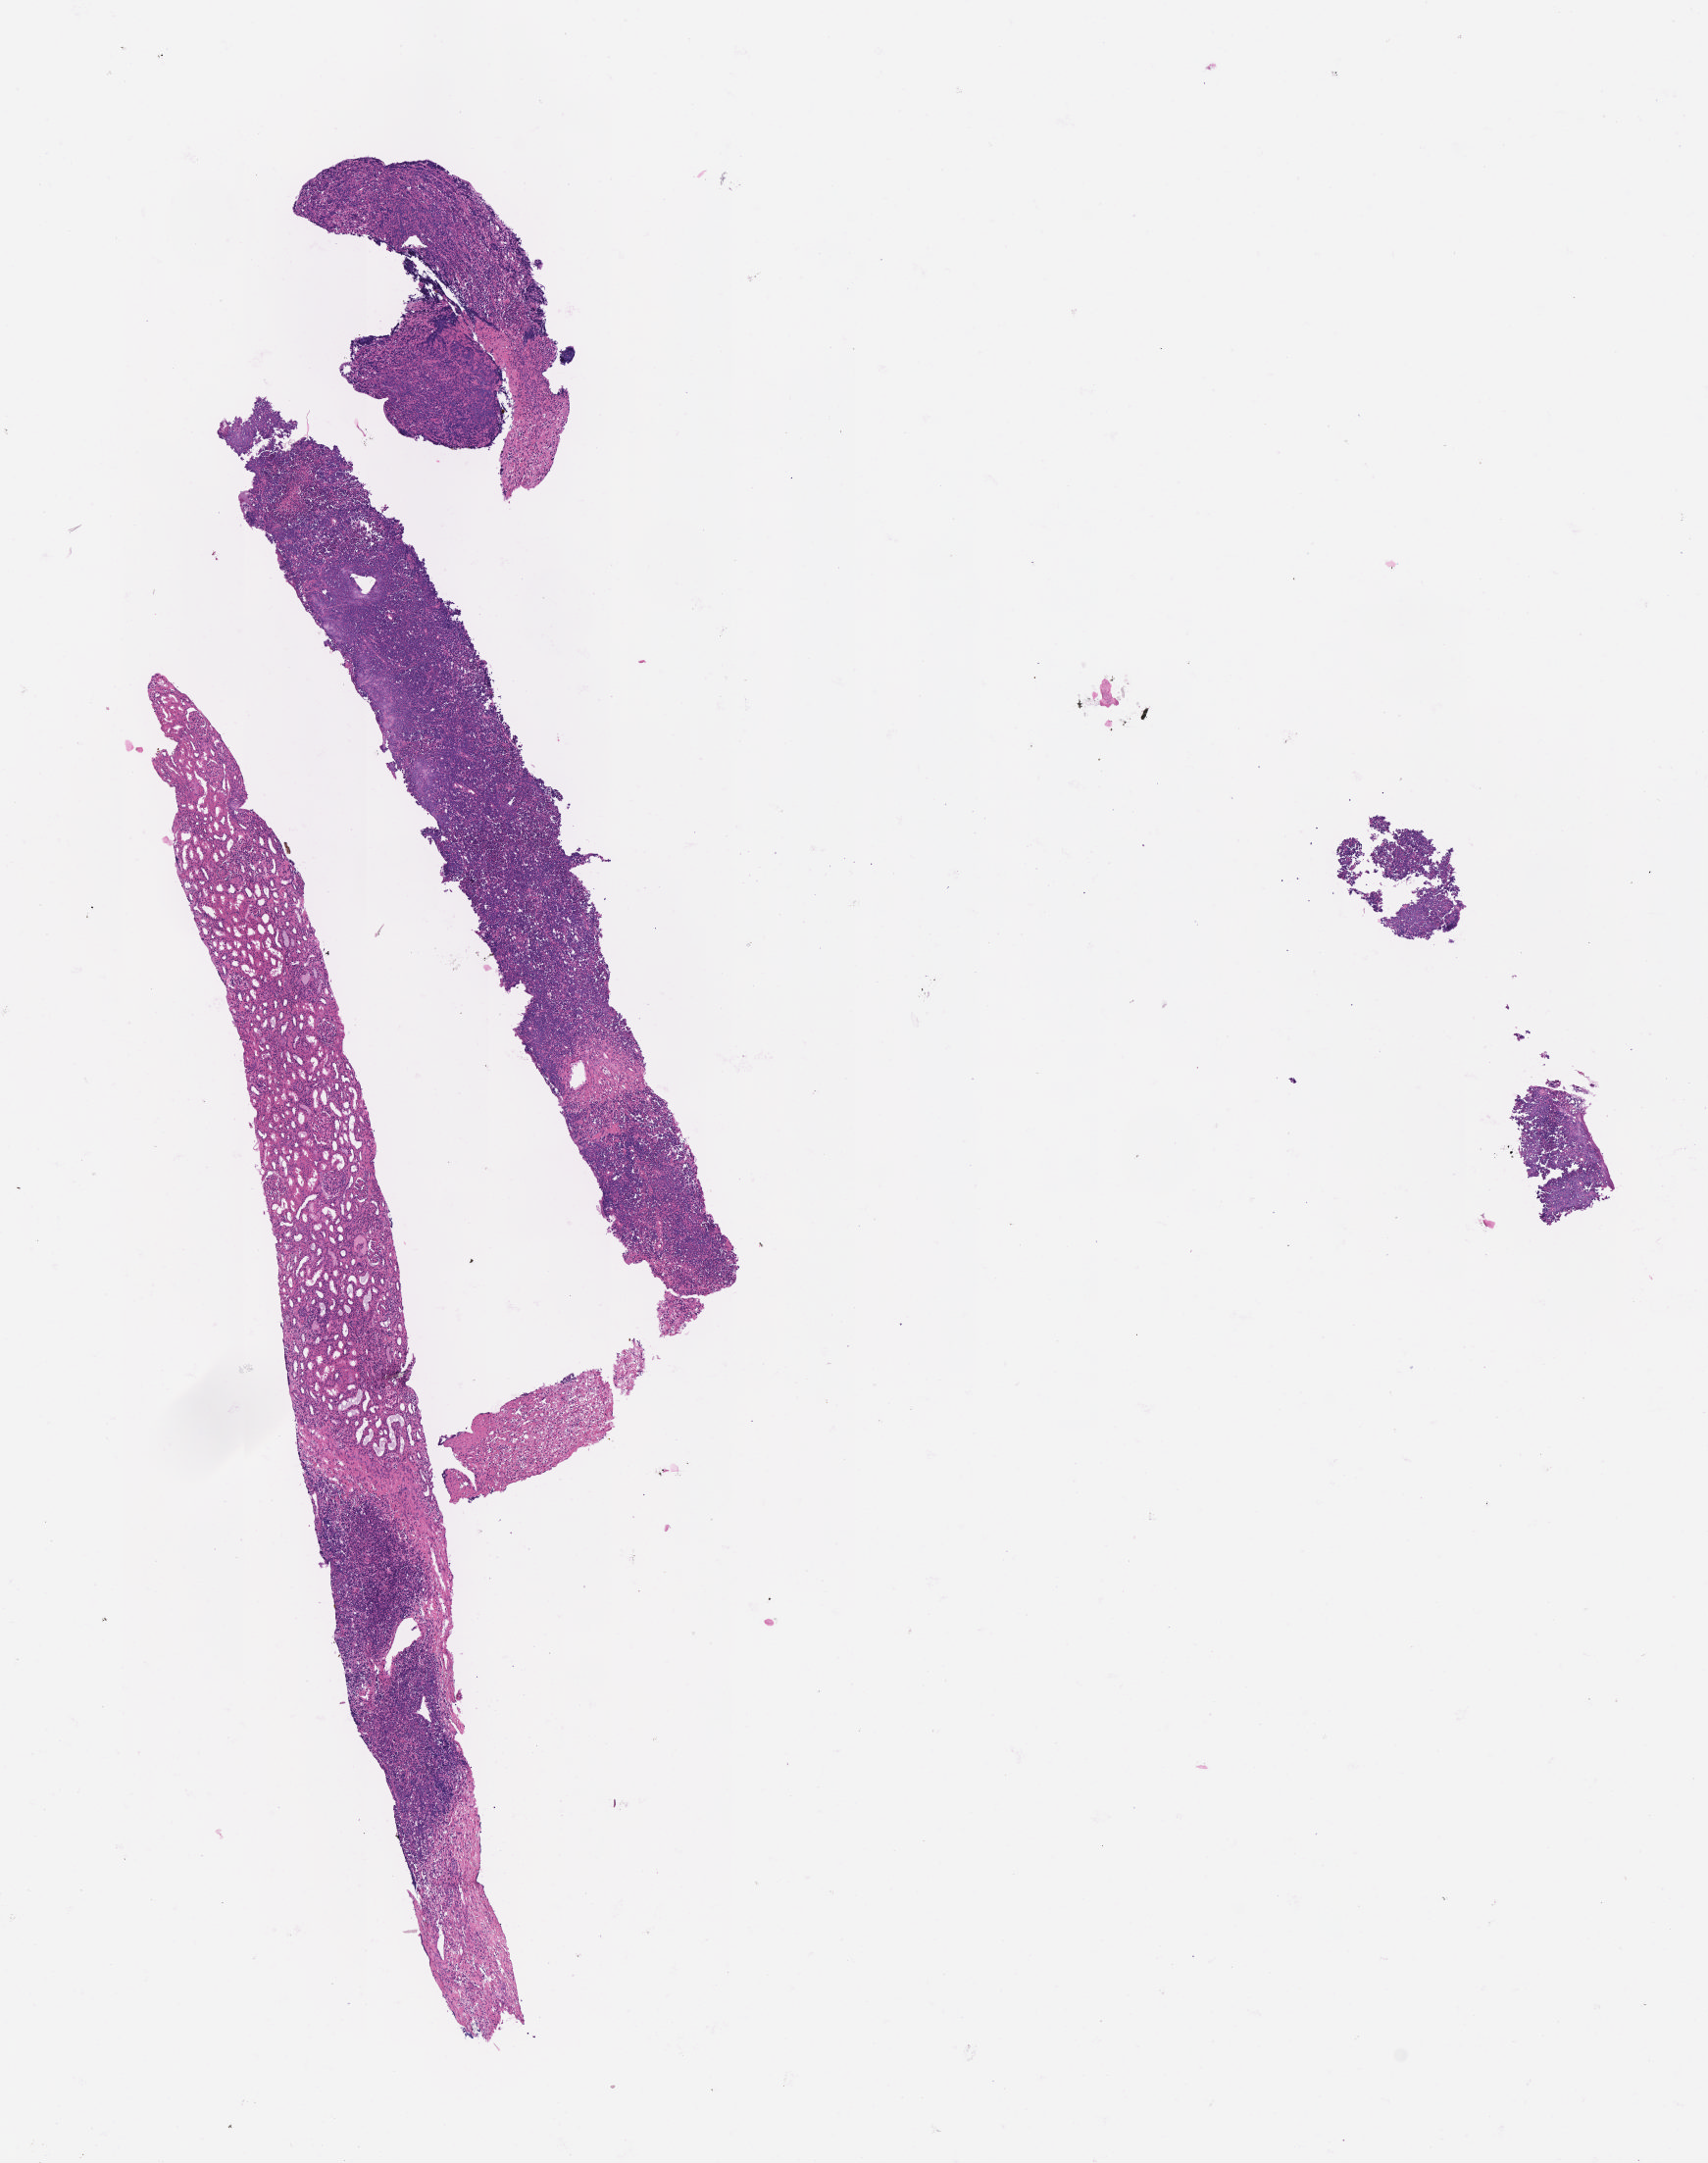
Digitized haematoxylin and eosin-stained section — a low-resolution overview of the entire scanned area, about 7.0 x 8.9 mm; formalin-fixed paraffin-embedded section; primary tumor; site: liver. Male patient; age at initial diagnosis 8 years. Pathologist review of this section (percent, as recorded): tumor cells 55%, tumor nuclei 80%.
Histologic diagnosis: Burkitt lymphoma, NOS.